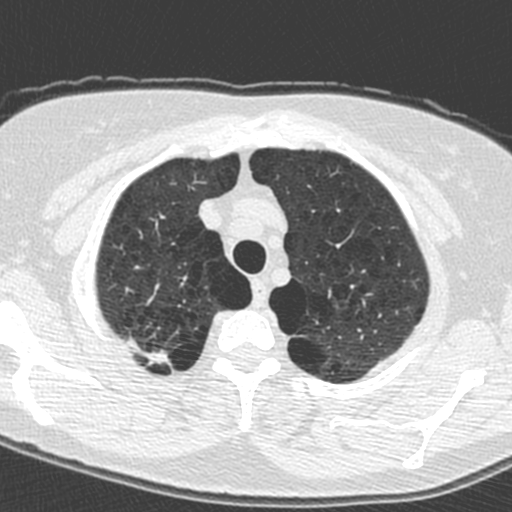
Axial slice from a low-dose chest CT screening exam; baseline annual screen; lung window (W 1500 / L -600 HU); 1.3 mm slice thickness; 120 kVp; 512 × 512 image matrix. Female participant, aged 59 years at enrolment. Current smoker at enrolment.
Expert-annotated lung lesion, bounding box [x1, y1, x2, y2] px = [132, 332, 177, 376]. Screening reader's record for this exam: no non-calcified nodule ≥4 mm recorded. Later outcome: lung cancer diagnosed 881 days after this screen — adenocarcinoma, NOS, right upper lobe, poorly differentiated (G3), stage IA (AJCC 6th edition), 20 mm at pathology.